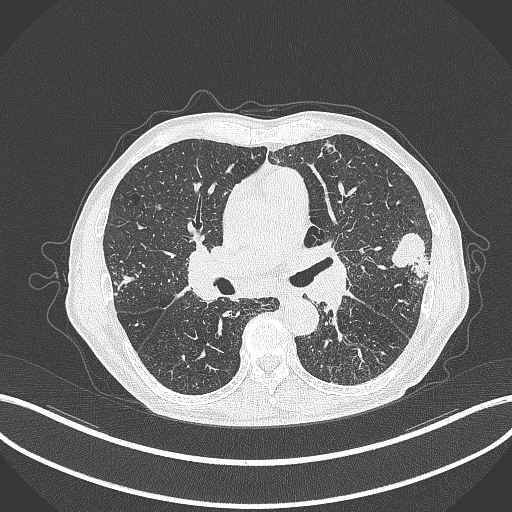
Chest CT, one axial slice. Position 229 of 463 along the scan axis. Reconstruction kernel B70f. 120 kVp. Lung window (W 1500 / L -600 HU). 1 mm slice thickness. 512 × 512 image matrix. Male patient, age 74 years. From the clinical record (not read from this slice): clinical TNM (as recorded): T2a N1 M0.
Outlined on this slice (rectangle marked by the reading radiologist):
- lung tumour (recorded histology: adenocarcinoma): box from (x=390, y=230) to (x=430, y=280) px